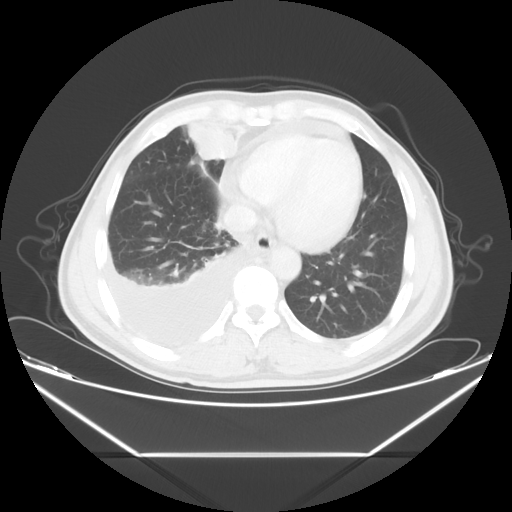
Chest CT, one axial slice. Position 16 of 56 along the scan axis. Reconstruction kernel STANDARD. 120 kVp. Lung window (W 1500 / L -600 HU). 5 mm slice thickness. 512 × 512 image matrix, field of view 412 × 412 mm. Male patient, age 57 years. Case-level facts recorded for this patient, not image findings: clinical TNM (as recorded): T2 N3 M1.
Outlined on this slice (rectangle marked by the reading radiologist):
- lung tumour (recorded histology: adenocarcinoma): bounding box (x1, y1, x2, y2) in pixels: (190, 115, 242, 165)